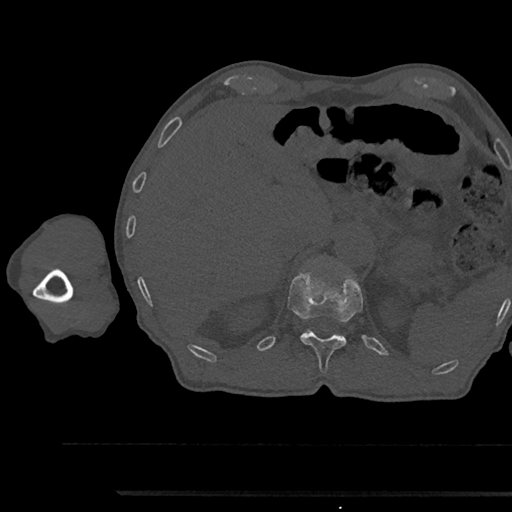
CT including the spine, one axial slice. Position 702 of 797 along the scan axis. Reconstruction kernel Br40s/3. Bone window (W 1800 / L 400 HU). 512 × 512 image matrix. Male patient, age 79 years. Case-level facts recorded for this patient, not image findings: primary cancer: prostate.
Structures marked on this image (semi-automatically segmented with operator editing):
- T12 vertebra: bounding box <288,273,362,372> (left, top, right, bottom; pixels)